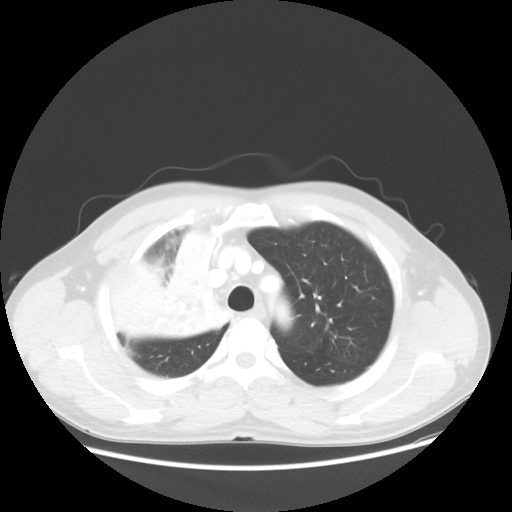
Chest CT, one axial slice. Slice 42 of 56 in the series (ordered by position). Reconstruction kernel STANDARD. Lung window (W 1500 / L -600 HU). 512 × 512 image matrix, field of view 398 × 398 mm. Male patient, age 60 years. From the clinical record (not read from this slice): clinical TNM (as recorded): T2a N1 M0.
Outlined on this slice (bounding box drawn by a radiologist):
- lung tumour (recorded histology: squamous cell carcinoma): box from (x=139, y=224) to (x=234, y=340) px